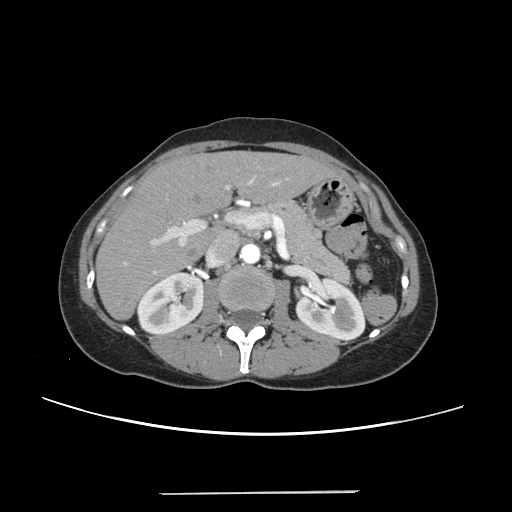
Contrast-enhanced abdominal CT, one axial slice; position 129 of 240 along the scan axis; 120 kVp; soft-tissue window (W 400 / L 40 HU); 1.25 mm slice thickness; 512 × 512 image matrix, field of view 371 × 371 mm. Female patient, age 60 years. From the clinical record (not read from this slice): diagnosis: colorectal cancer liver metastases, imaged before liver resection; multiple liver metastases: no; largest metastasis: 1.5 cm; disease in both lobes: no.
Structures marked on this image (expert manual segmentation):
- liver: bounding box (x1, y1, x2, y2) in pixels: (98, 152, 333, 318)
- planned liver remnant (the part of the liver to remain after resection): (98, 152, 332, 319)
- portal vein (with intrahepatic branches): (125, 177, 289, 274)
- liver metastasis: (205, 165, 212, 171)